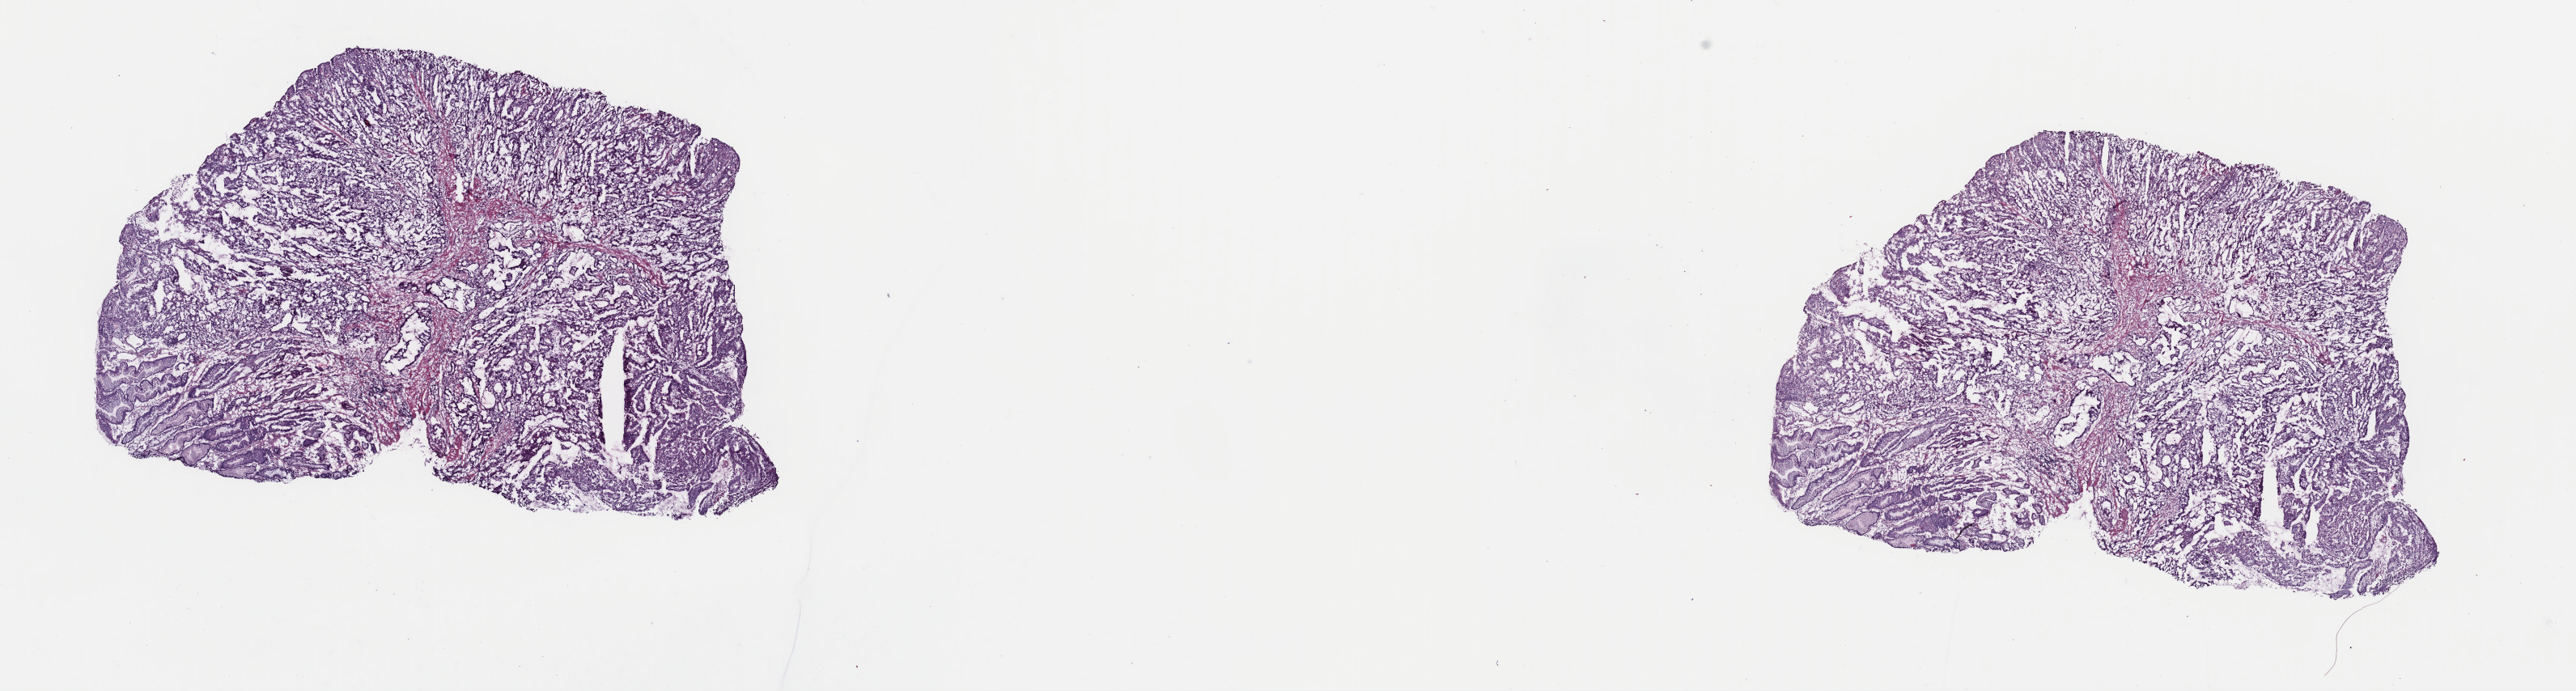
Whole-slide histology image, H&E, a low-resolution overview of the entire scanned area, about 25.1 x 6.7 mm (acquisition: 40x scan). Frozen section from the top of the tissue portion. Primary tumour sample from the stomach. Male, age 54 years at initial diagnosis. Histologic grade: G2 (moderately differentiated). Pathologist review of this section (percent, as recorded): tumour cells 87%, tumour nuclei 85%, normal cells 0%, stromal cells 12%, necrosis 1%. Infiltration values recorded for this section: lymphocyte infiltration 1%, monocyte infiltration 1%, neutrophil infiltration 1%.
* diagnosis: Tubular adenocarcinoma (gastric antrum)
* lymph nodes positive (case pathology): 5 of 53 examined
* AJCC pathologic stage: IIB (7th edition)